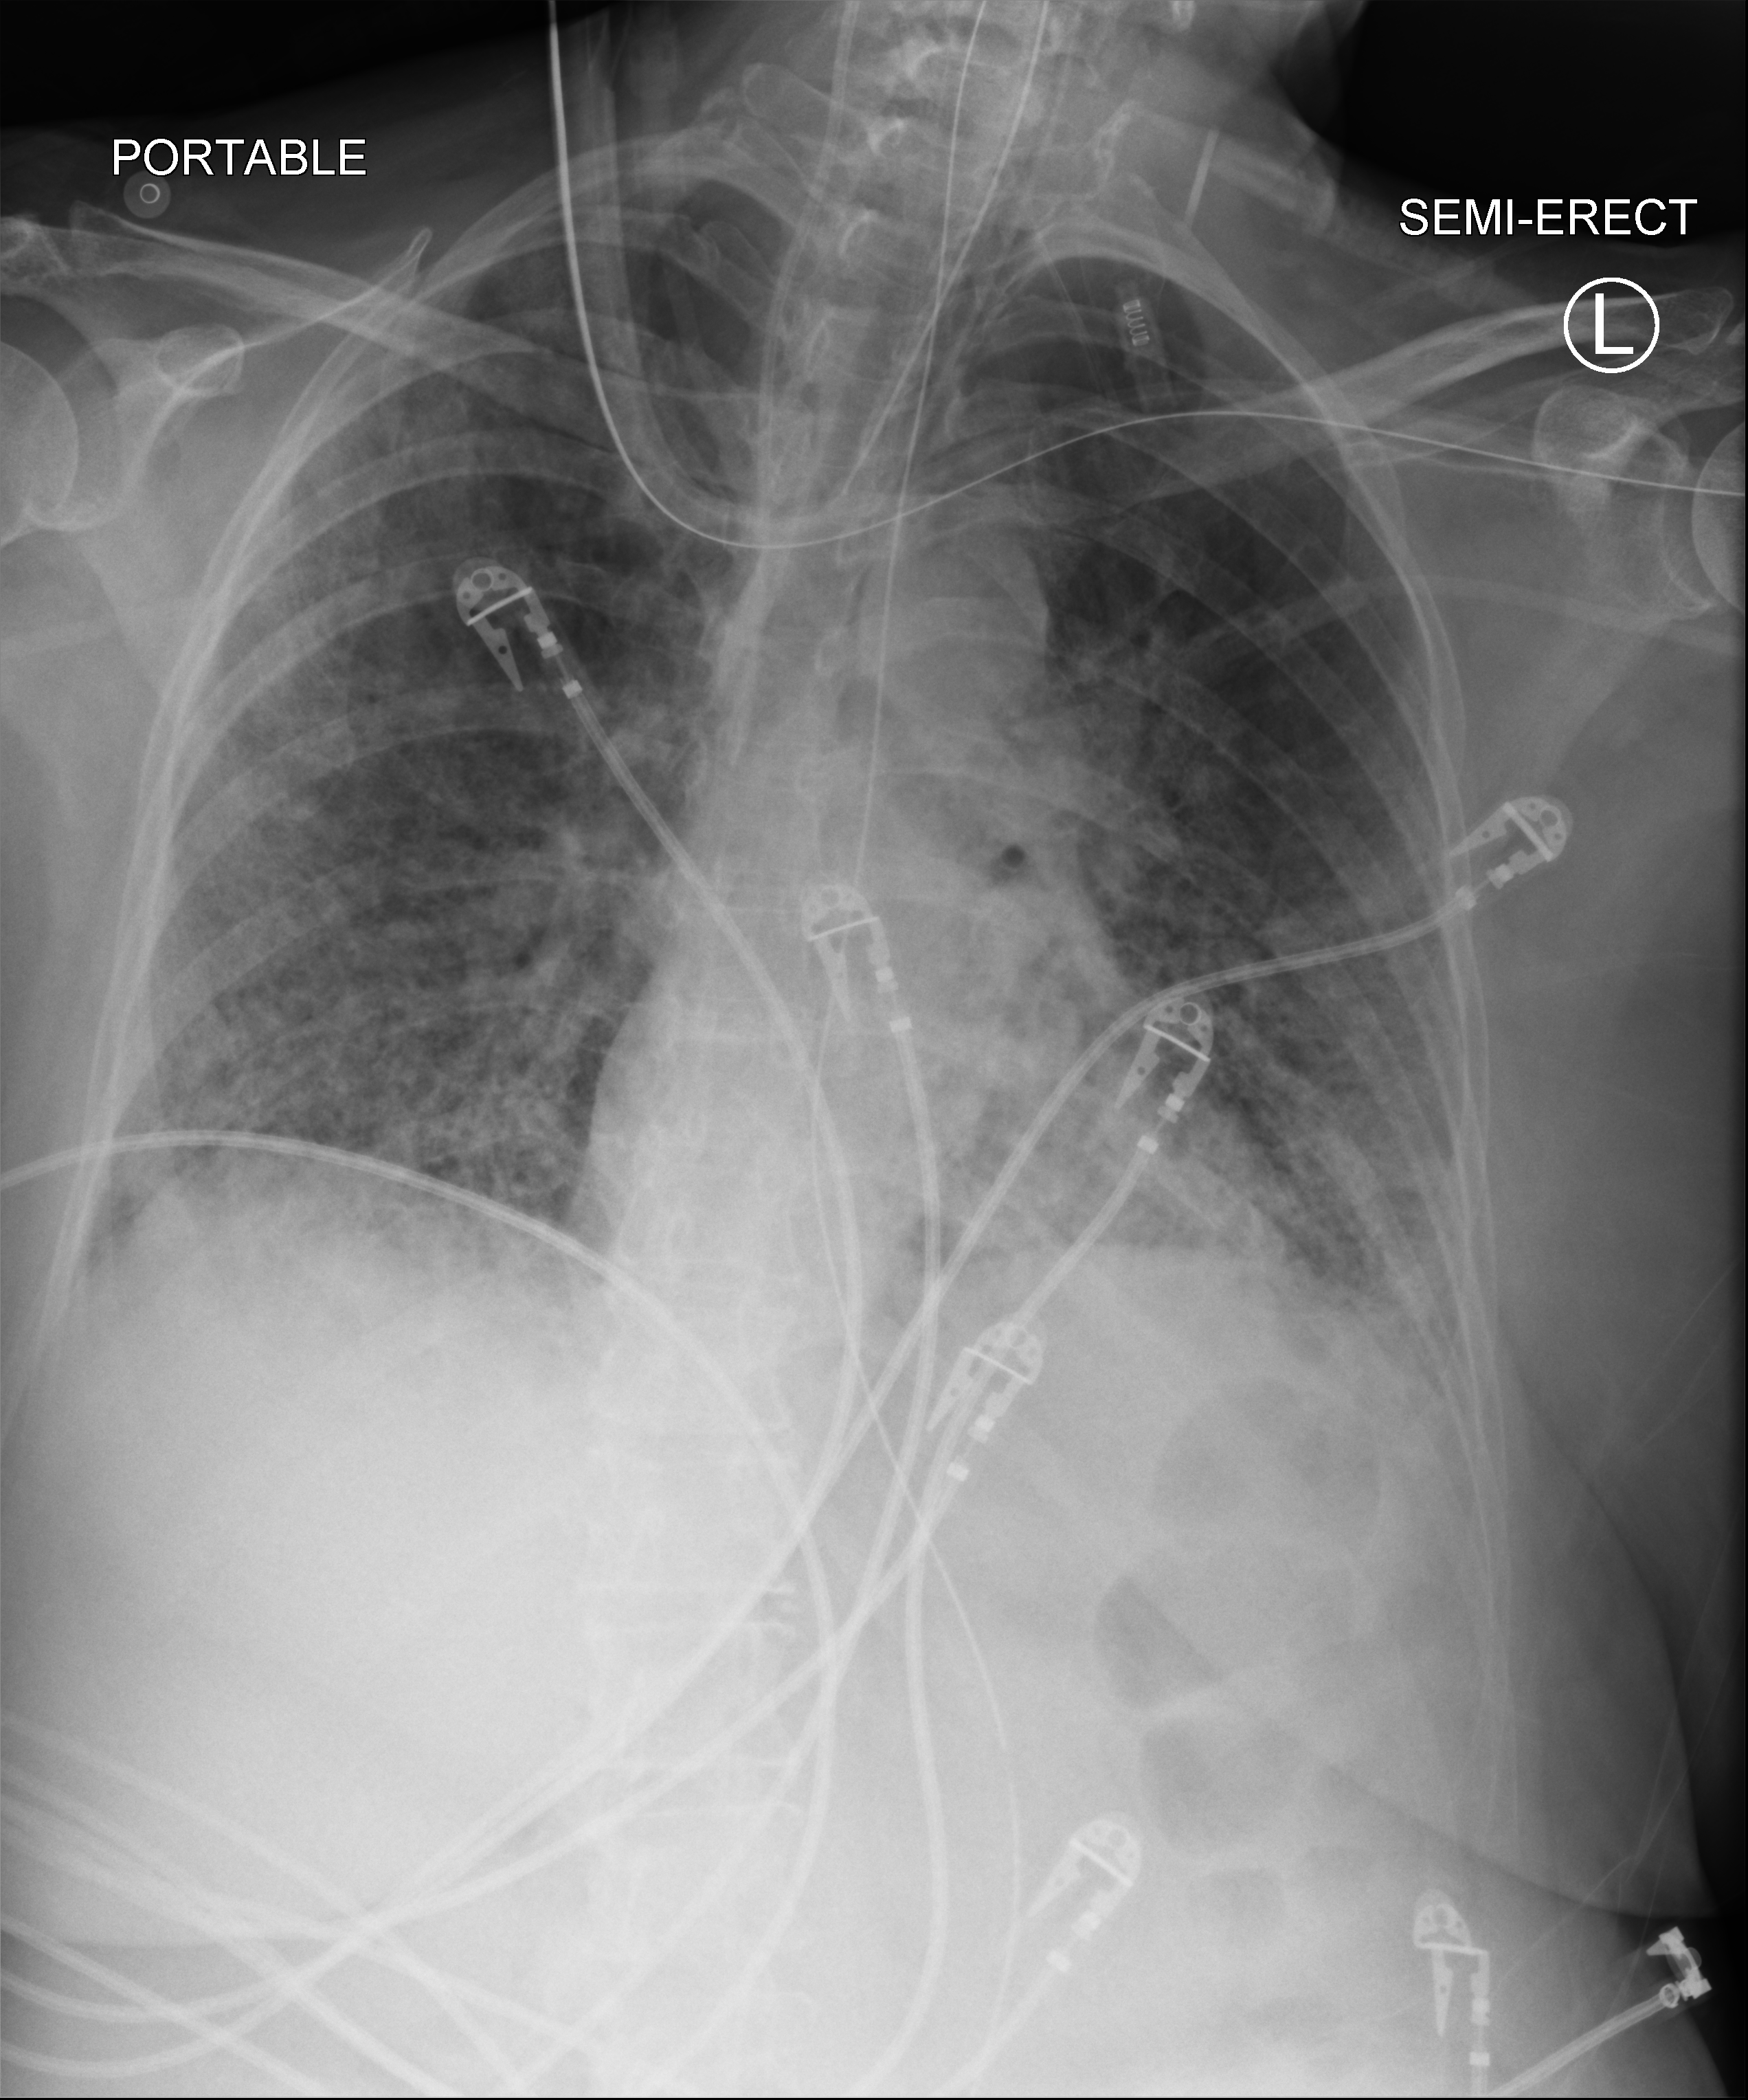
Portable chest radiograph, anteroposterior (AP) projection. Patient hospitalised with COVID-19; female, aged 60–74 years.
Admission-level facts for this patient (not findings on this image; timing relative to this image not recorded): mechanically ventilated during this hospital stay: yes; COPD (admission record): no.